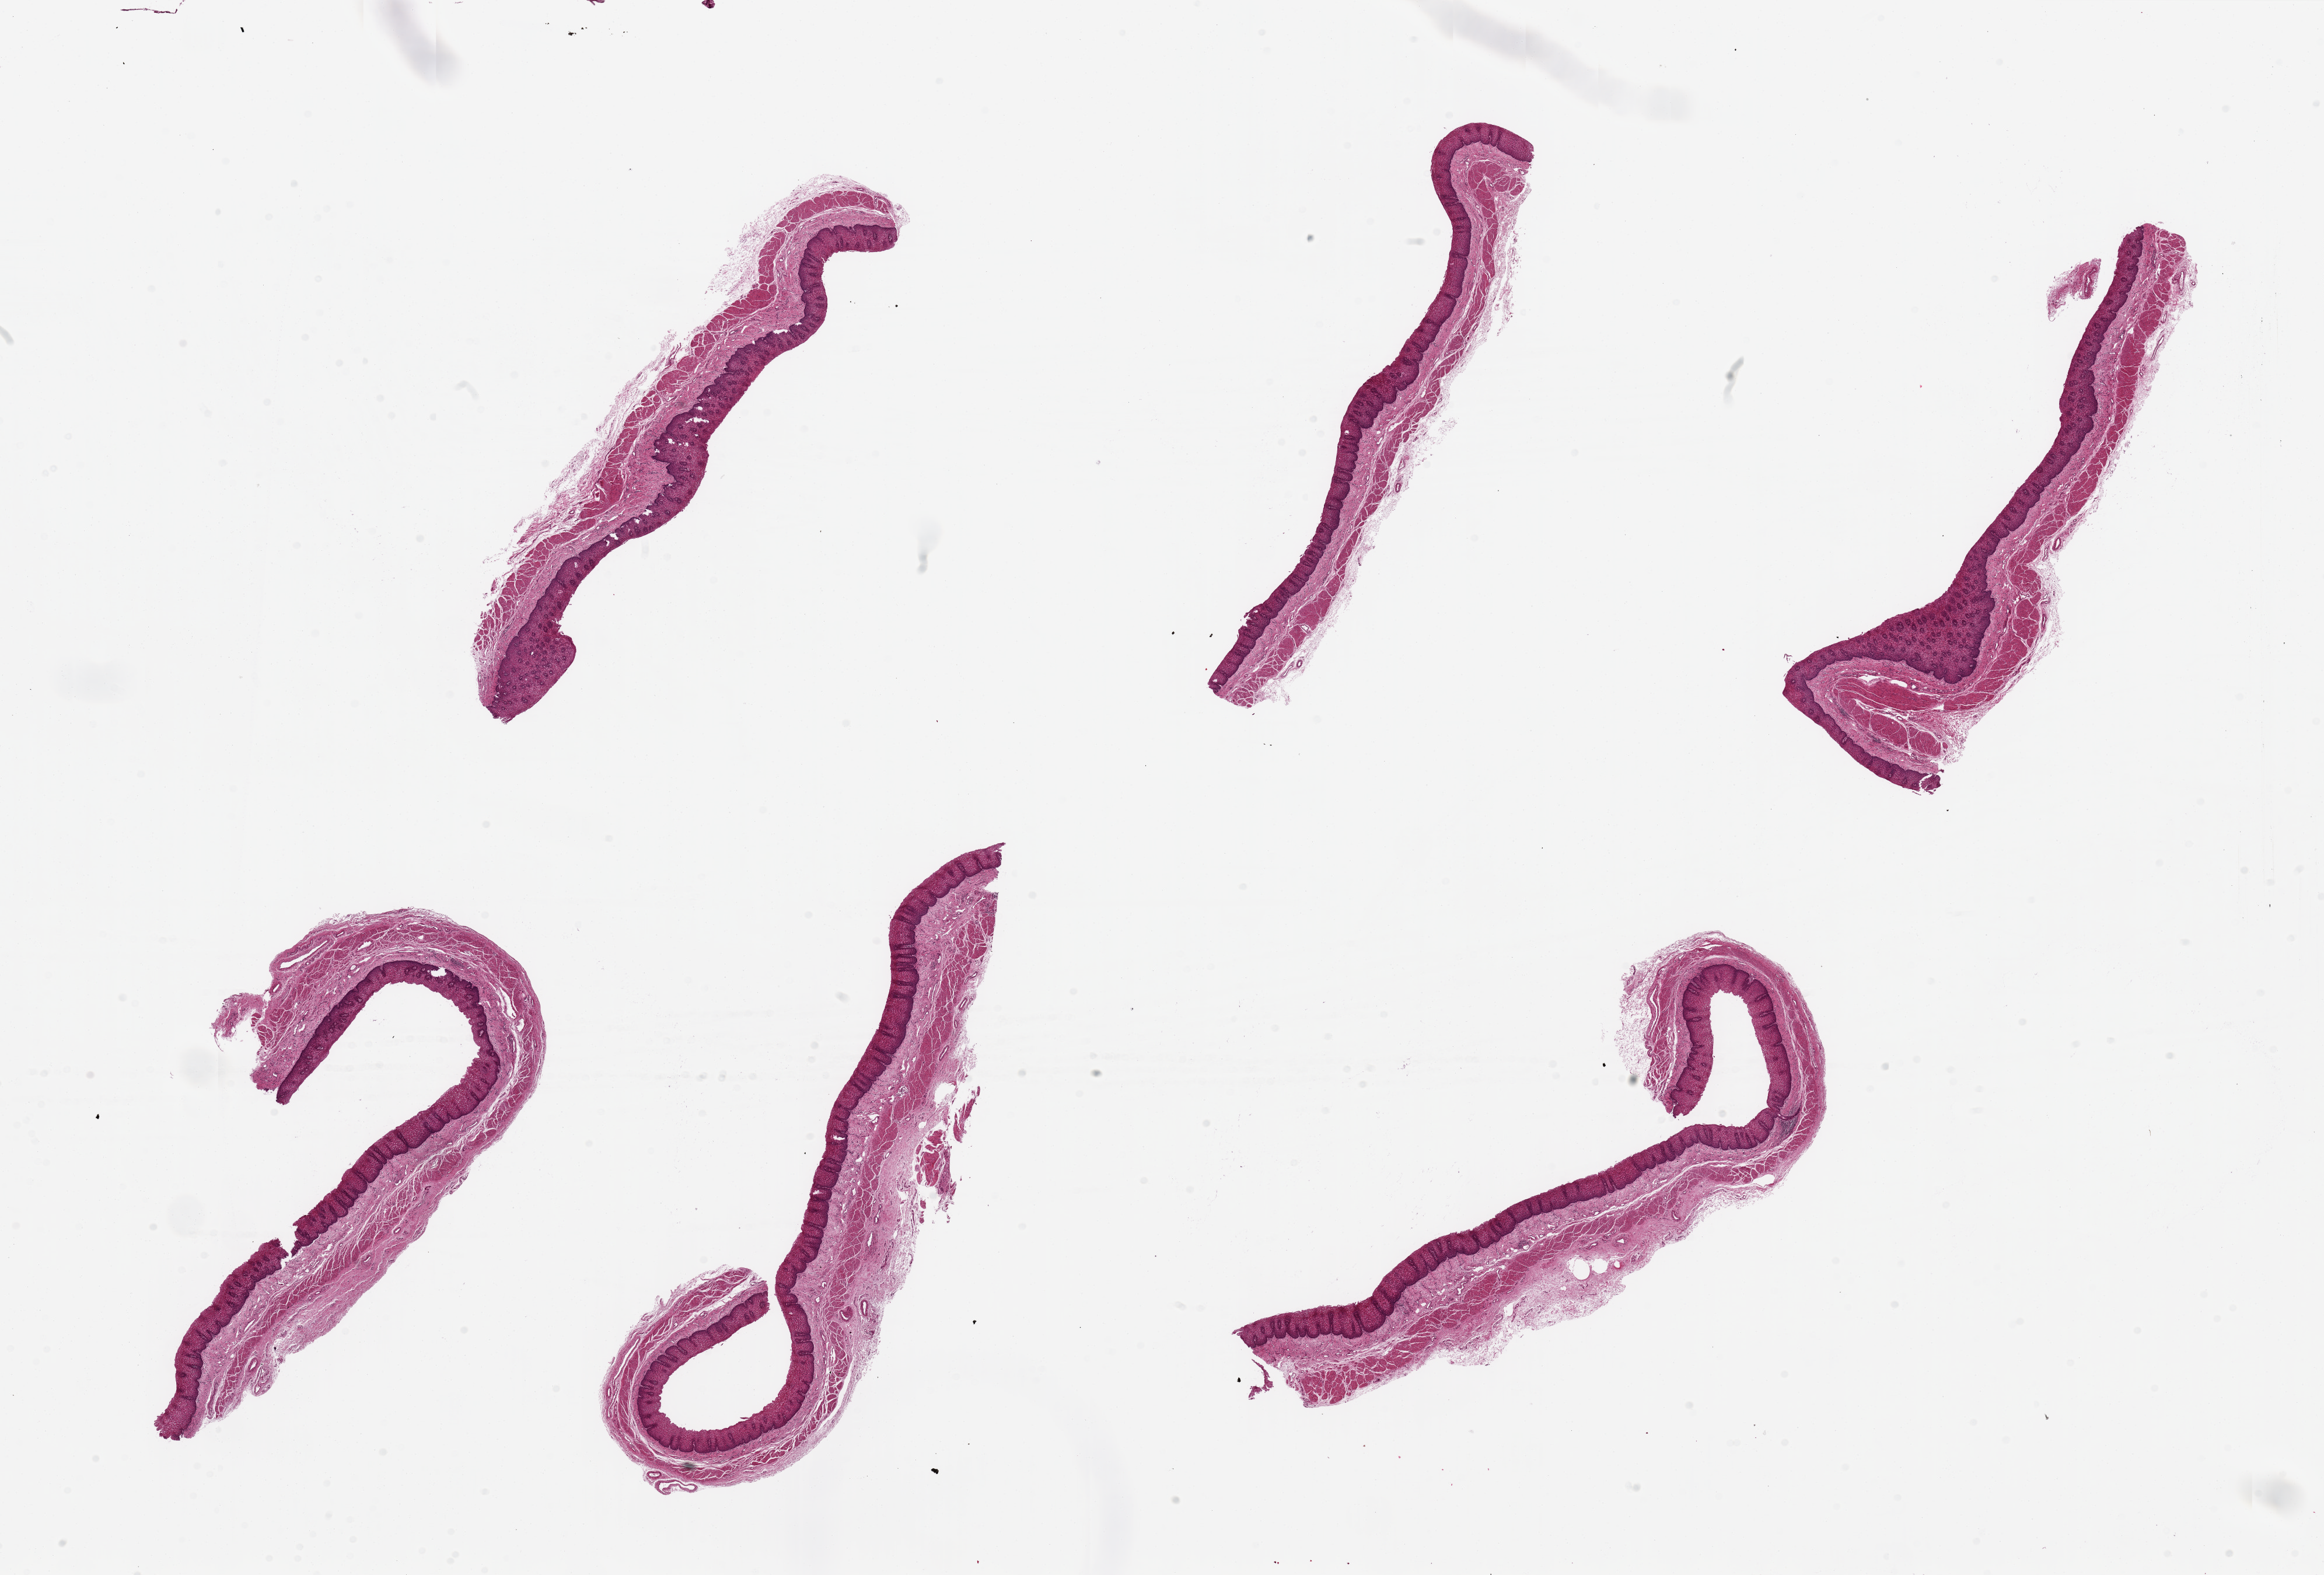
Haematoxylin and eosin whole-slide image, whole scanned area (about 31.5 x 21.3 mm, slide scanned at 20x) shown as a low-resolution overview; PAXgene-fixed paraffin-embedded (PFPE) section; sampled site (target tissue): esophageal mucous membrane; tissue donor sample. Donor: female.
Review note (as recorded): 6 pieces, up to 10x5mm; ~40% squamous mucosa.